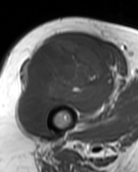
MRI of an extremity soft-tissue mass, one axial slice; MR volume resampled by the dataset authors to the PET/CT grid (not the native acquisition matrix); 138 × 172 image matrix, field of view 135 × 168 mm. Female patient. Case-level facts recorded for this patient, not image findings: histological type: pleiomorphic undifferentiated sarcoma; grade: high; site of the primary tumour: right quadricep.
Outlined on this slice (expert contour drawn on MRI and transferred to this co-registered scan by the dataset authors):
- gross tumour volume including surrounding oedema: box from (x=19, y=39) to (x=109, y=126) px
- gross tumour volume (mass): (x=19, y=39)–(x=109, y=126)